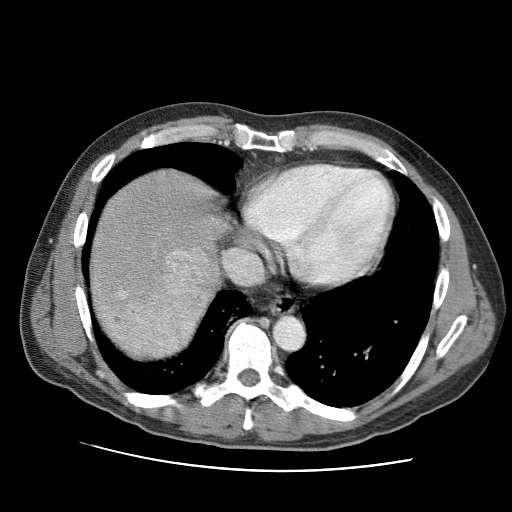
Contrast-enhanced abdominal CT (liver protocol), one axial slice; position 85 of 95 along the scan axis; reconstruction kernel STANDARD; 120 kVp; one of 2 acquisitions stored at this slice position; soft-tissue window (W 400 / L 40 HU); 2.5 mm slice thickness; 512 × 512 image matrix, field of view 360 × 360 mm. From the clinical record (not read from this slice): diagnosis: hepatocellular carcinoma (patient treated with transarterial chemoembolisation; whether this scan precedes or follows treatment is not stated here); TNM stage (as recorded): Stage-IVA; Child-Pugh class: A; tumour nodularity: multinodular.
Outlined on this slice (semi-automatically segmented with operator editing):
- liver parenchyma outside the tumour (the mass and vessels are separate outlines, so this box may not span the whole liver): bounding box [x1, y1, x2, y2] px = [92, 170, 230, 329]
- mass: [103, 247, 218, 360]
- liver vessels: [160, 262, 184, 319]